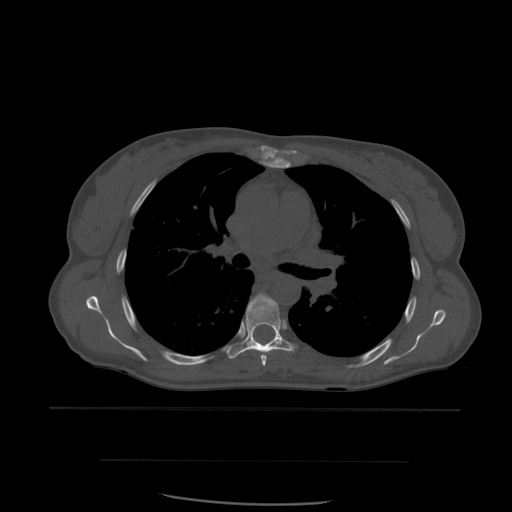
CT including the spine, one axial slice; slice 397 of 574 in the series (ordered by position); bone window (W 1800 / L 400 HU); 1.25 mm slice thickness; 512 × 512 image matrix, field of view 392 × 392 mm. Patient age 48 years. Case-level facts recorded for this patient, not image findings: primary cancer: lung; vertebrae with lytic lesions (as recorded): T11.
Annotated regions visible in this slice (semi-automatically segmented with operator editing):
- T5 vertebra: bounding box [x1, y1, x2, y2] px = [261, 354, 267, 367]
- T6 vertebra: [227, 294, 295, 359]